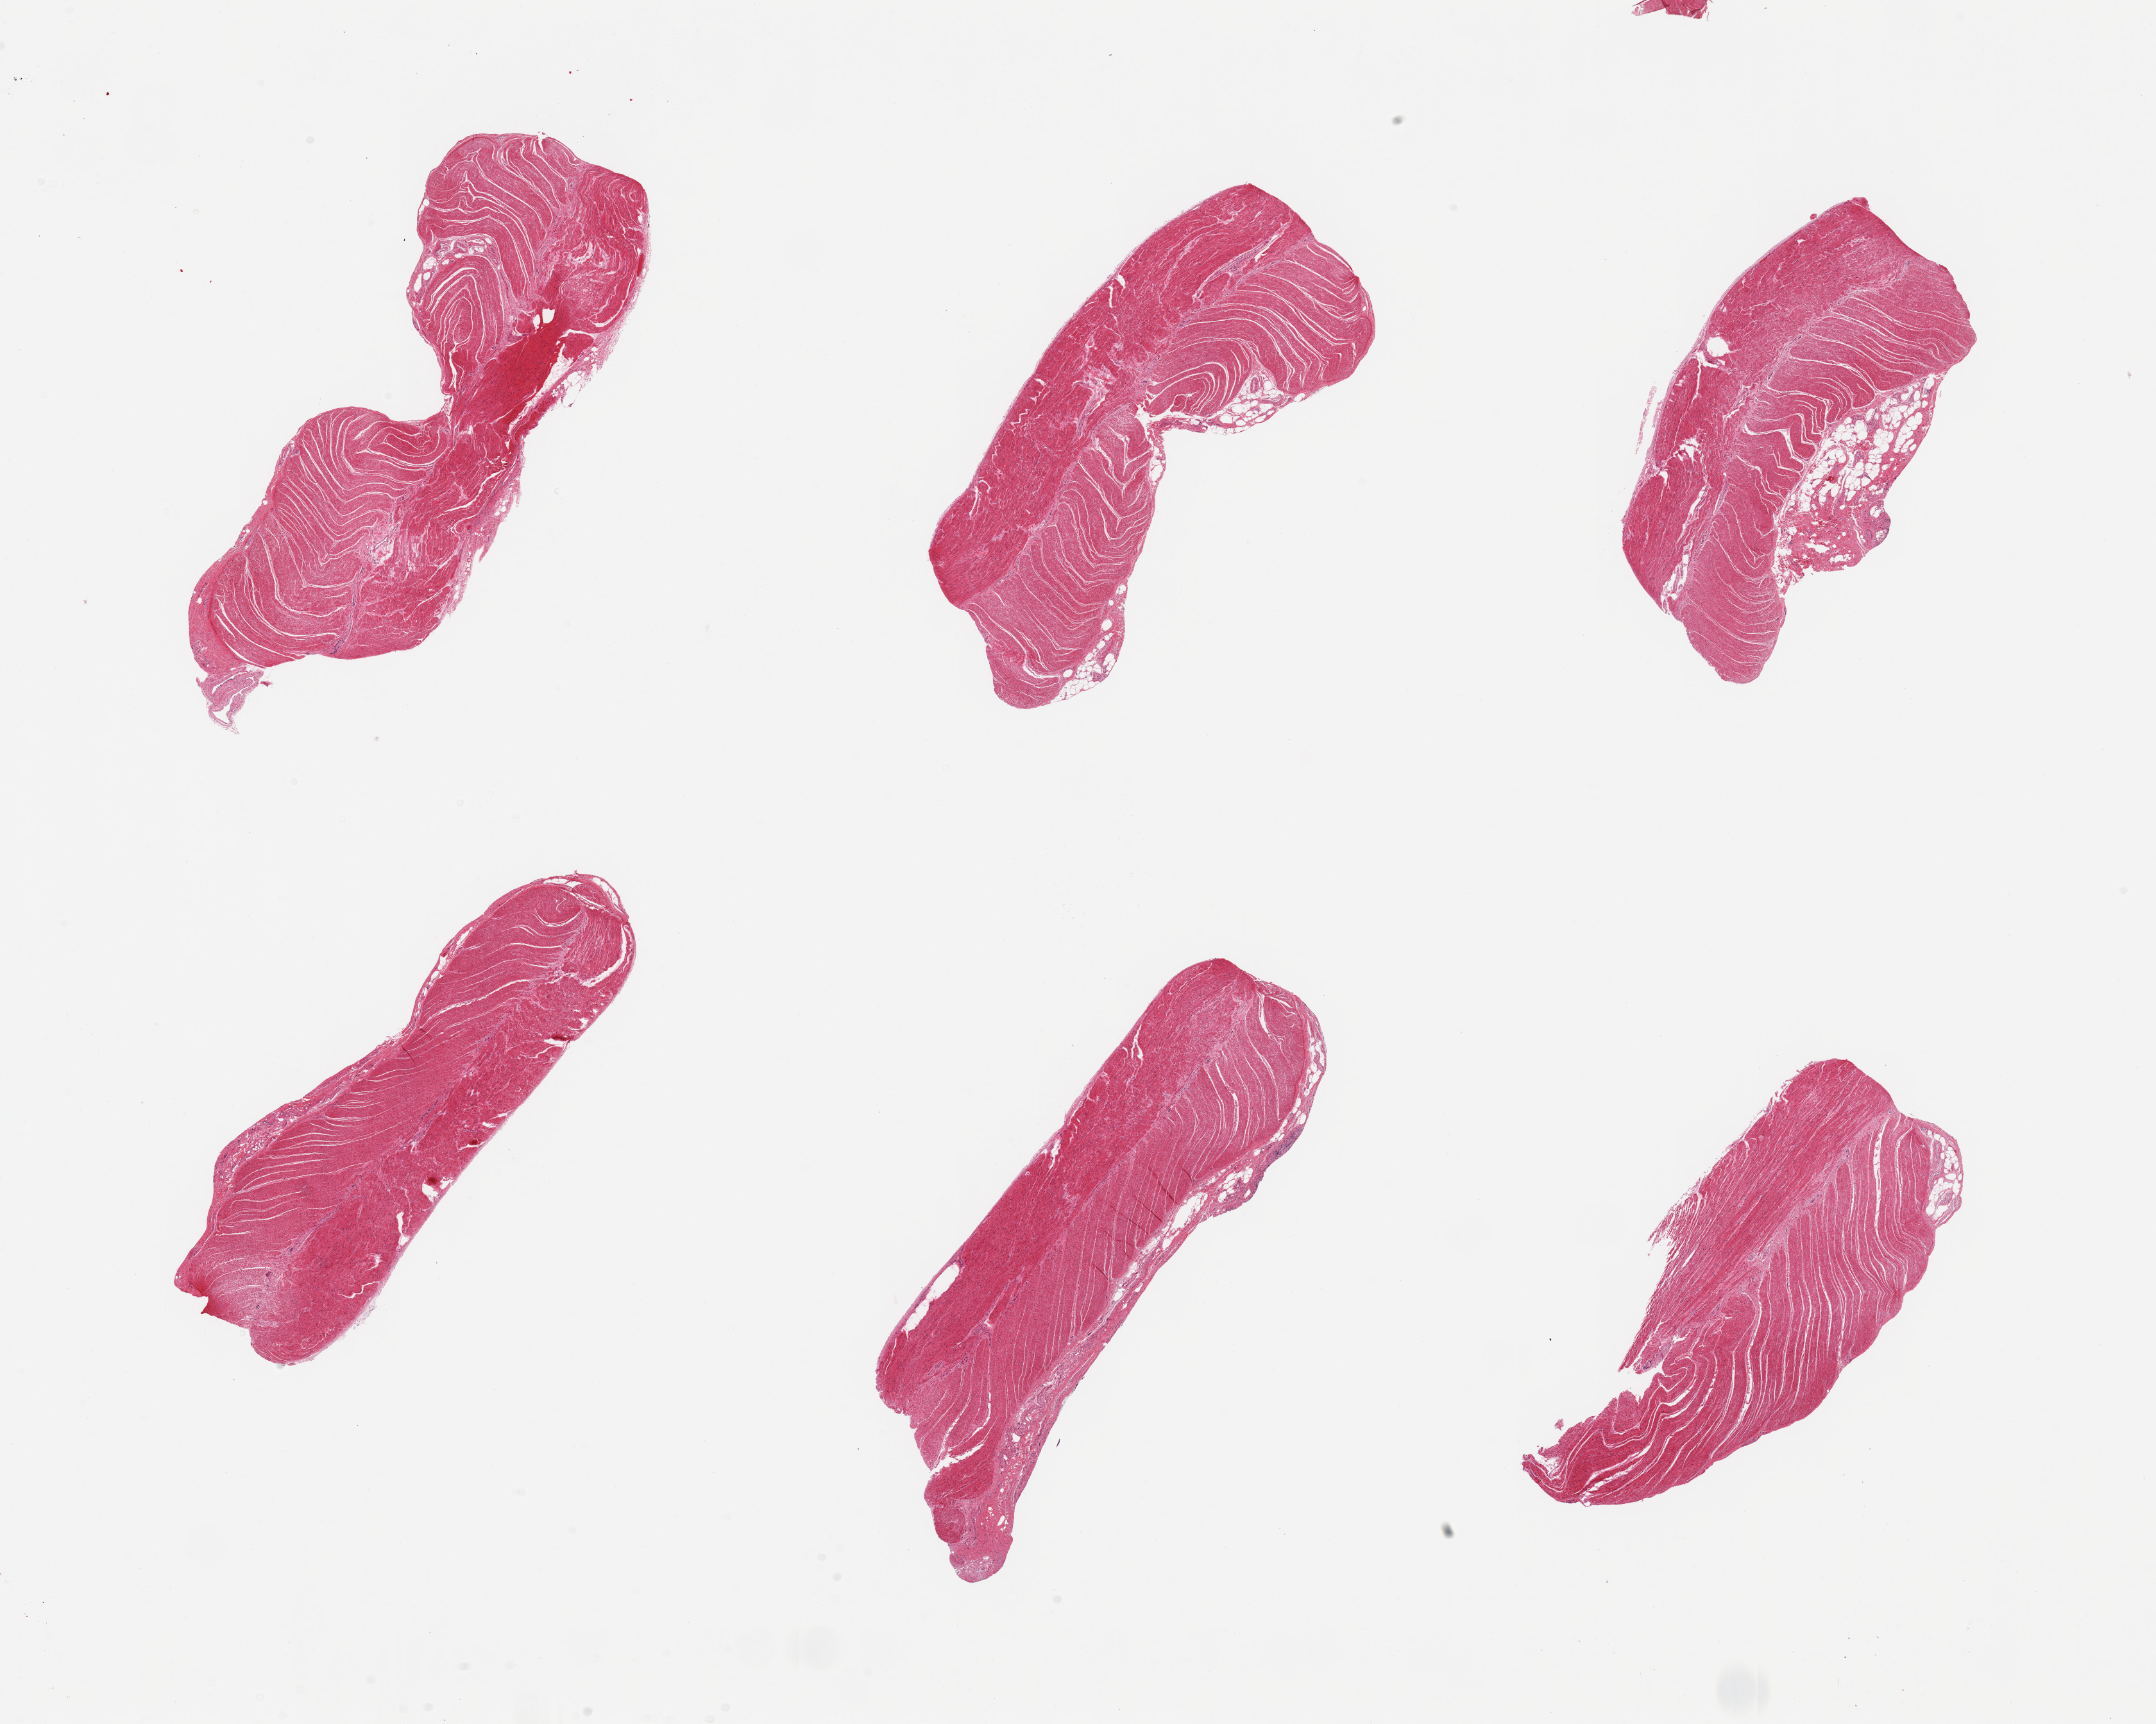
Whole-slide image, H&E stain, whole scanned area (about 26.6 x 21.2 mm, acquisition: 20x scan) shown as a low-resolution overview; PAXgene-fixed paraffin-embedded (PFPE) section; target tissue: sigmoid colon; tissue donor sample. Donor: male.
Reviewer comment on this tissue sample: 6 pieces, confirmed target muscularis.